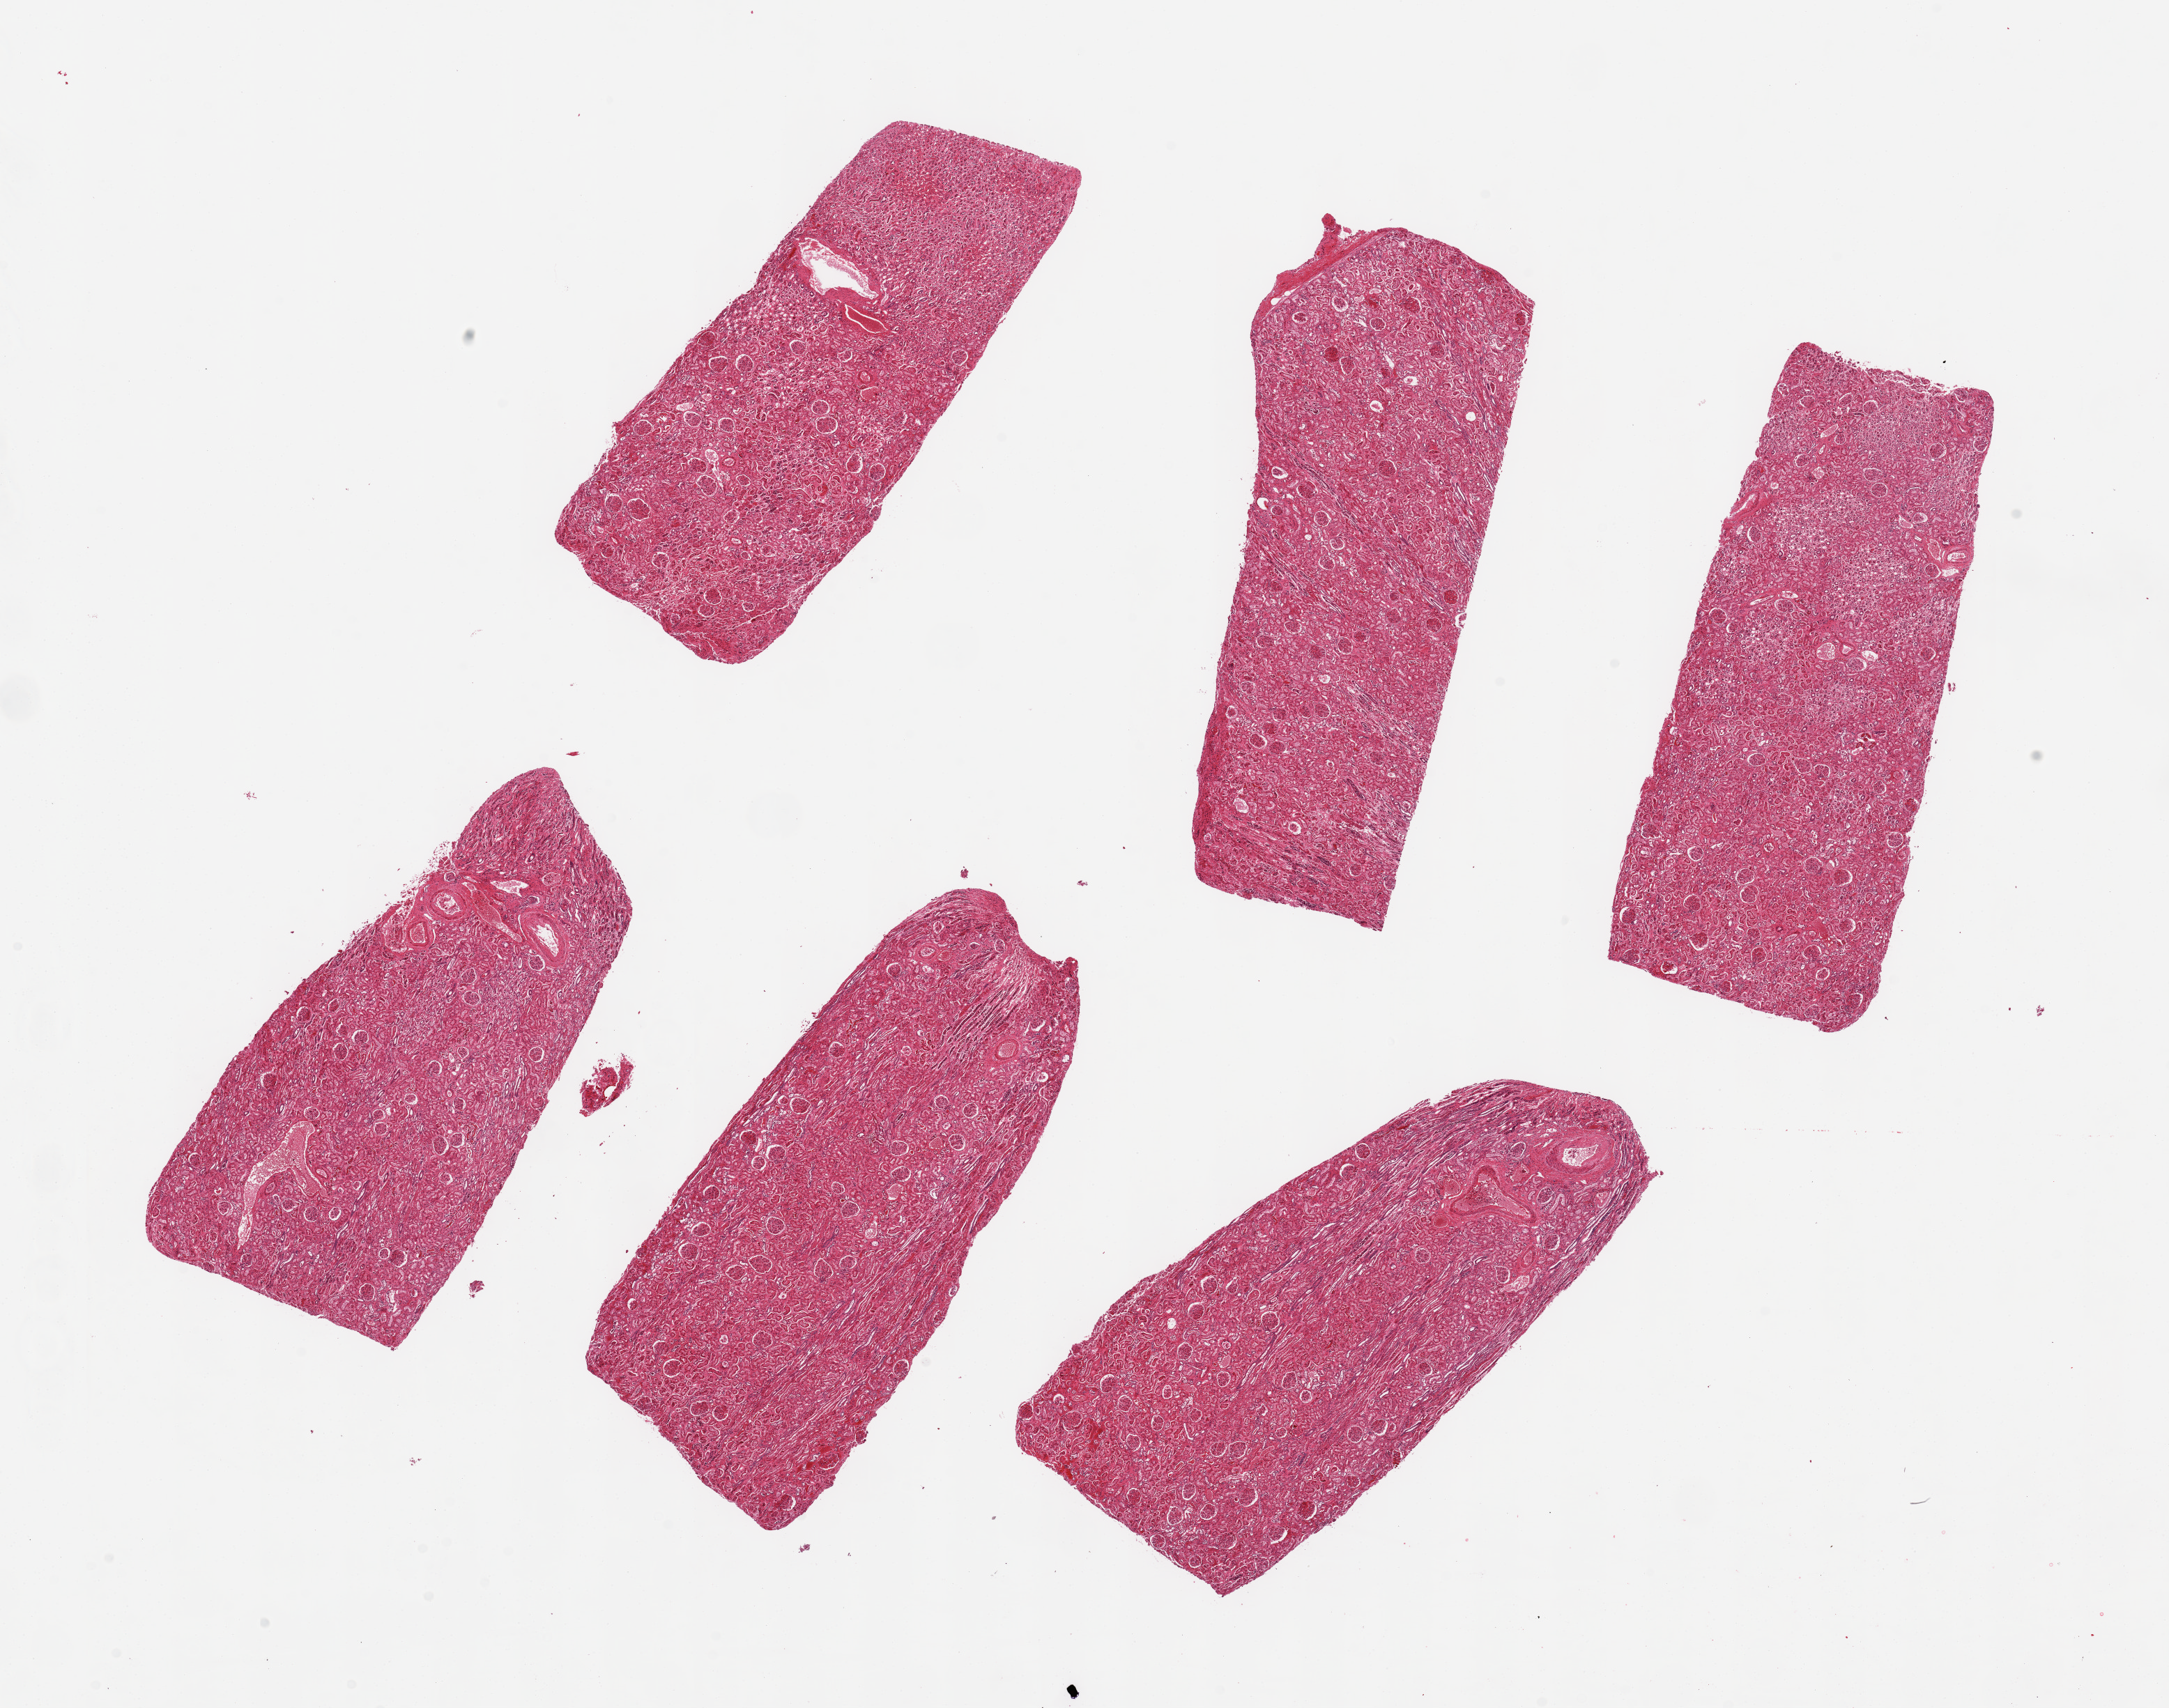
Haematoxylin and eosin whole-slide image, low-resolution overview of the scanned area, about 24.6 x 19.4 mm. PAXgene-fixed paraffin-embedded (PFPE) section. Section of renal cortex (target tissue). Tissue donor sample. Donor: male.
* review note (as recorded): 6 pieces up to 7.7x3.5 mm; hyperemia and red cell casts